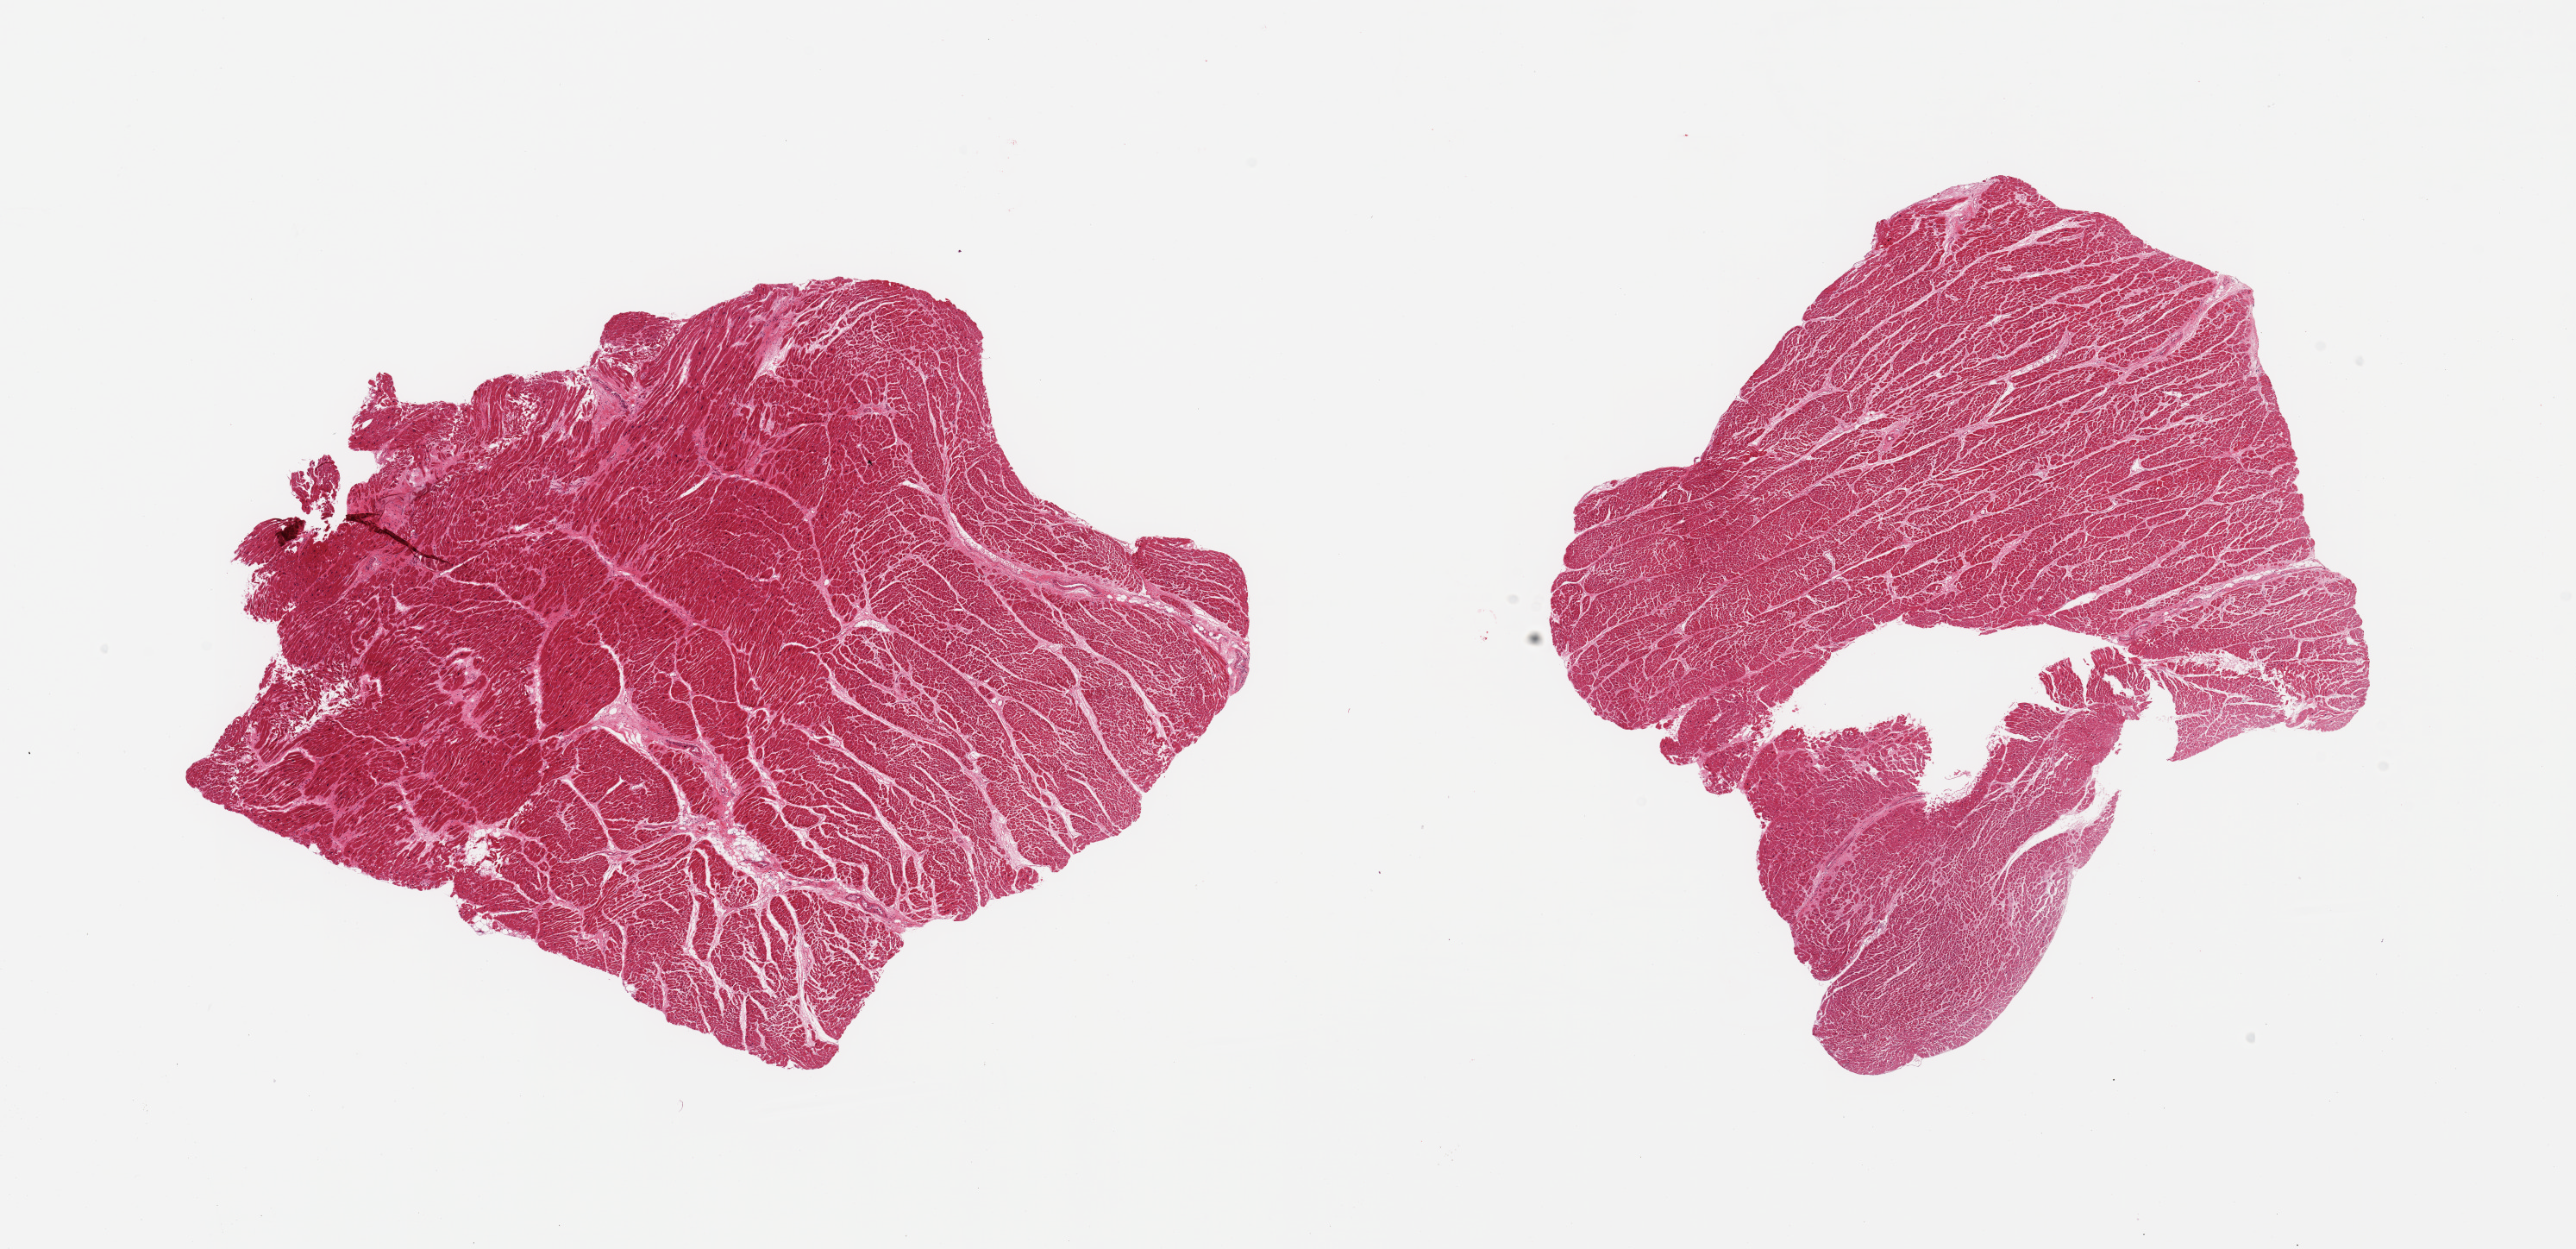
Hematoxylin and eosin (H&E) whole-slide image, a low-resolution overview of the entire scanned area, about 23.6 x 11.5 mm (acquisition: 20x scan), PAXgene-fixed, paraffin-embedded tissue, section of heart (target tissue), tissue donor sample. Donor sex: male.
* pathologist's review note for this sample: 2 pieces, mild interstitial fibrosis/chronic ischemic changes